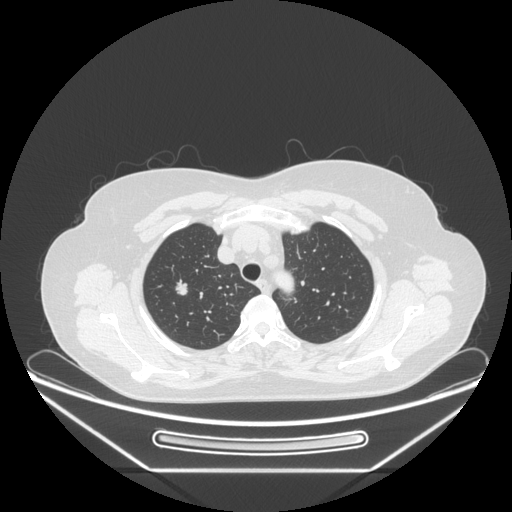
Chest CT, one axial slice. Slice 198 of 236 in the series (ordered by position). Lung window (W 1500 / L -600 HU). 512 × 512 image matrix, field of view 433 × 433 mm. Patient: female, 60 years. Case-level facts recorded for this patient, not image findings: clinical TNM (as recorded): T1c N0 M0; histopathological grade: G2-3.
Structures marked on this image (bounding box drawn by a radiologist):
- lung tumour (recorded histology: adenocarcinoma): bounding box (x1, y1, x2, y2) in pixels: (171, 274, 191, 300)